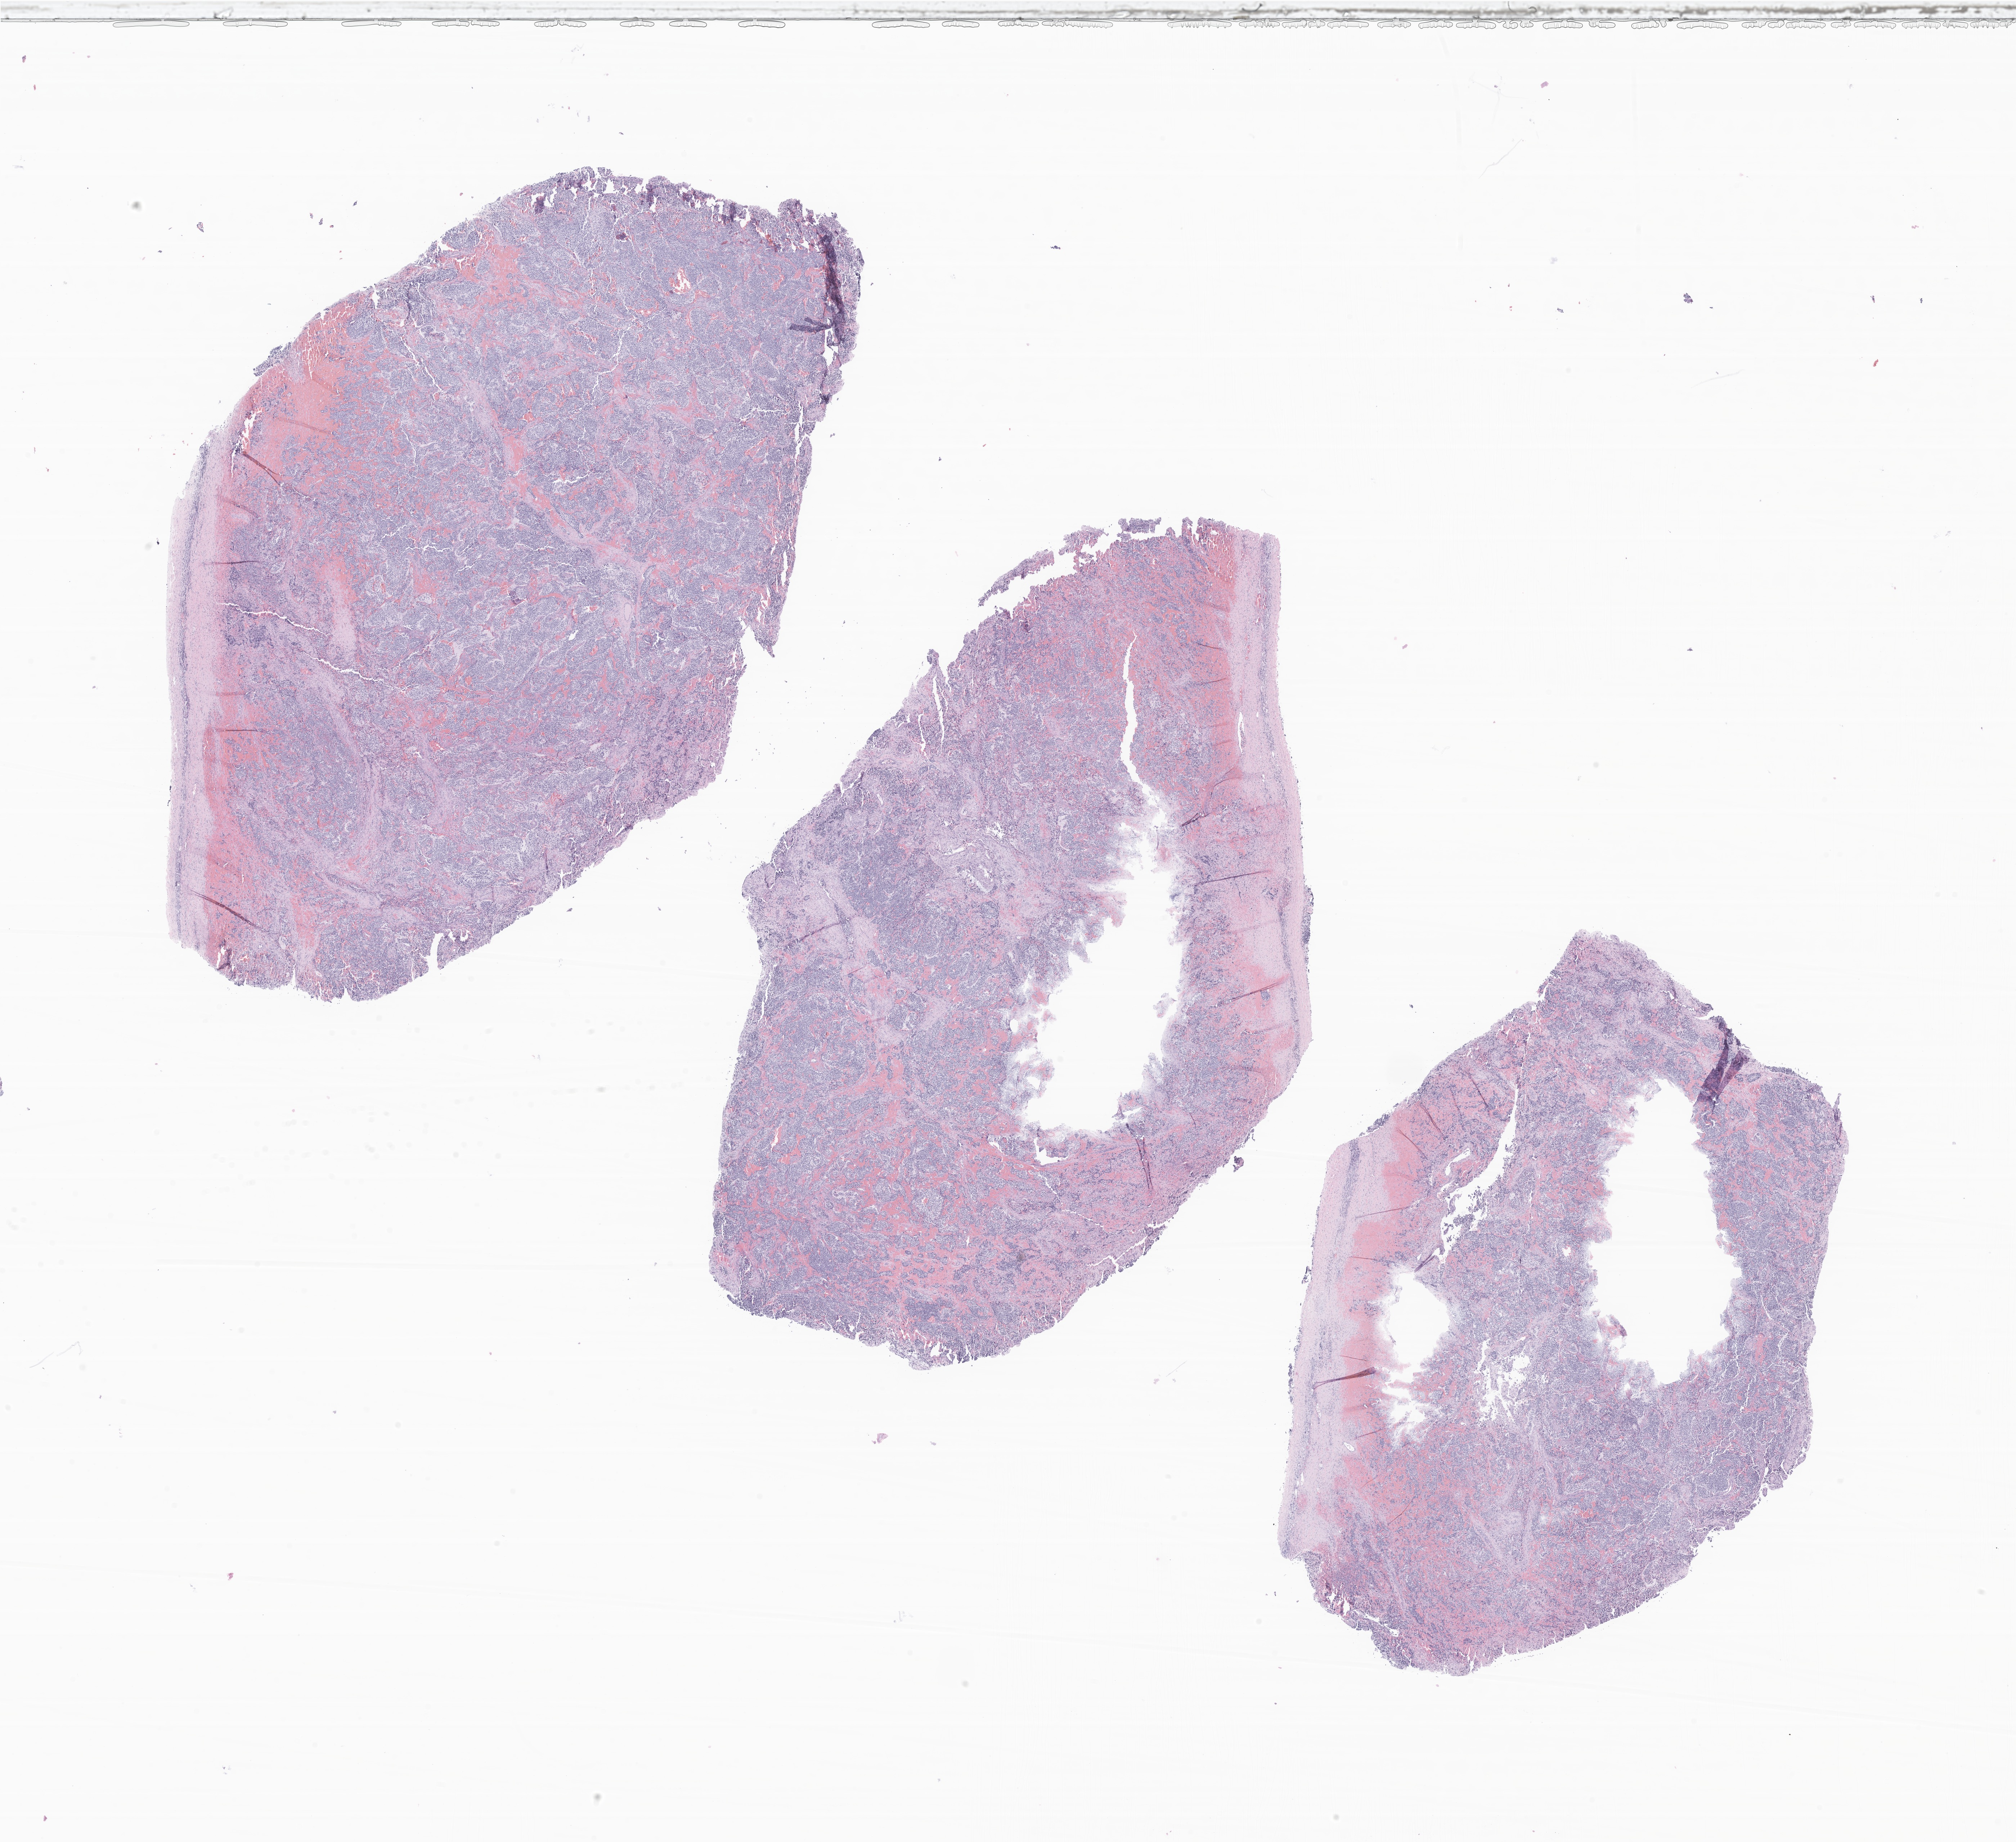
Haematoxylin and eosin whole-slide image of tumor tissue from the abdomen, a low-resolution overview of the entire scanned area, about 23.6 x 21.6 mm. Formalin-fixed, paraffin-embedded (FFPE) tissue. Patient male; age 409 days (about 1.1 years).
* recorded diagnosis: Neuroblastoma, NOS